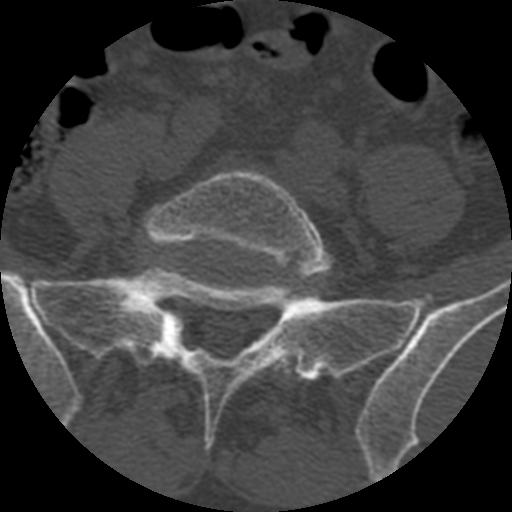
CT including the spine, one axial slice. Position 244 of 399 along the scan axis. Bone window (W 1800 / L 400 HU). 512 × 512 image matrix. Patient age 71 years. From the clinical record (not read from this slice): primary cancer: prostate.
Outlined on this slice (semi-automatically segmented with operator editing):
- L5 vertebra: bounding box <144,169,332,276> (left, top, right, bottom; pixels)